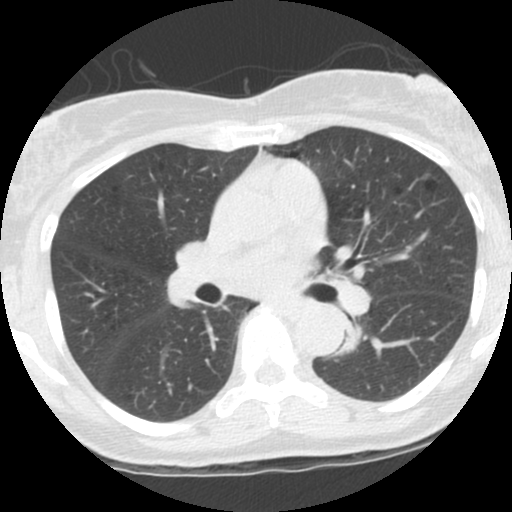
Low-dose screening chest CT, one axial slice. Slice 62 of 115 in the series (ordered by position). Reconstruction kernel STANDARD. Lung window (W 1500 / L -600 HU). 2.5 mm slice thickness. 512 × 512 image matrix.
Outlined on this slice (outlined manually by an expert reader):
- lesion 1 (tumor, lower lobe of left lung): bounding box (x1, y1, x2, y2) in pixels: (341, 336, 360, 353)